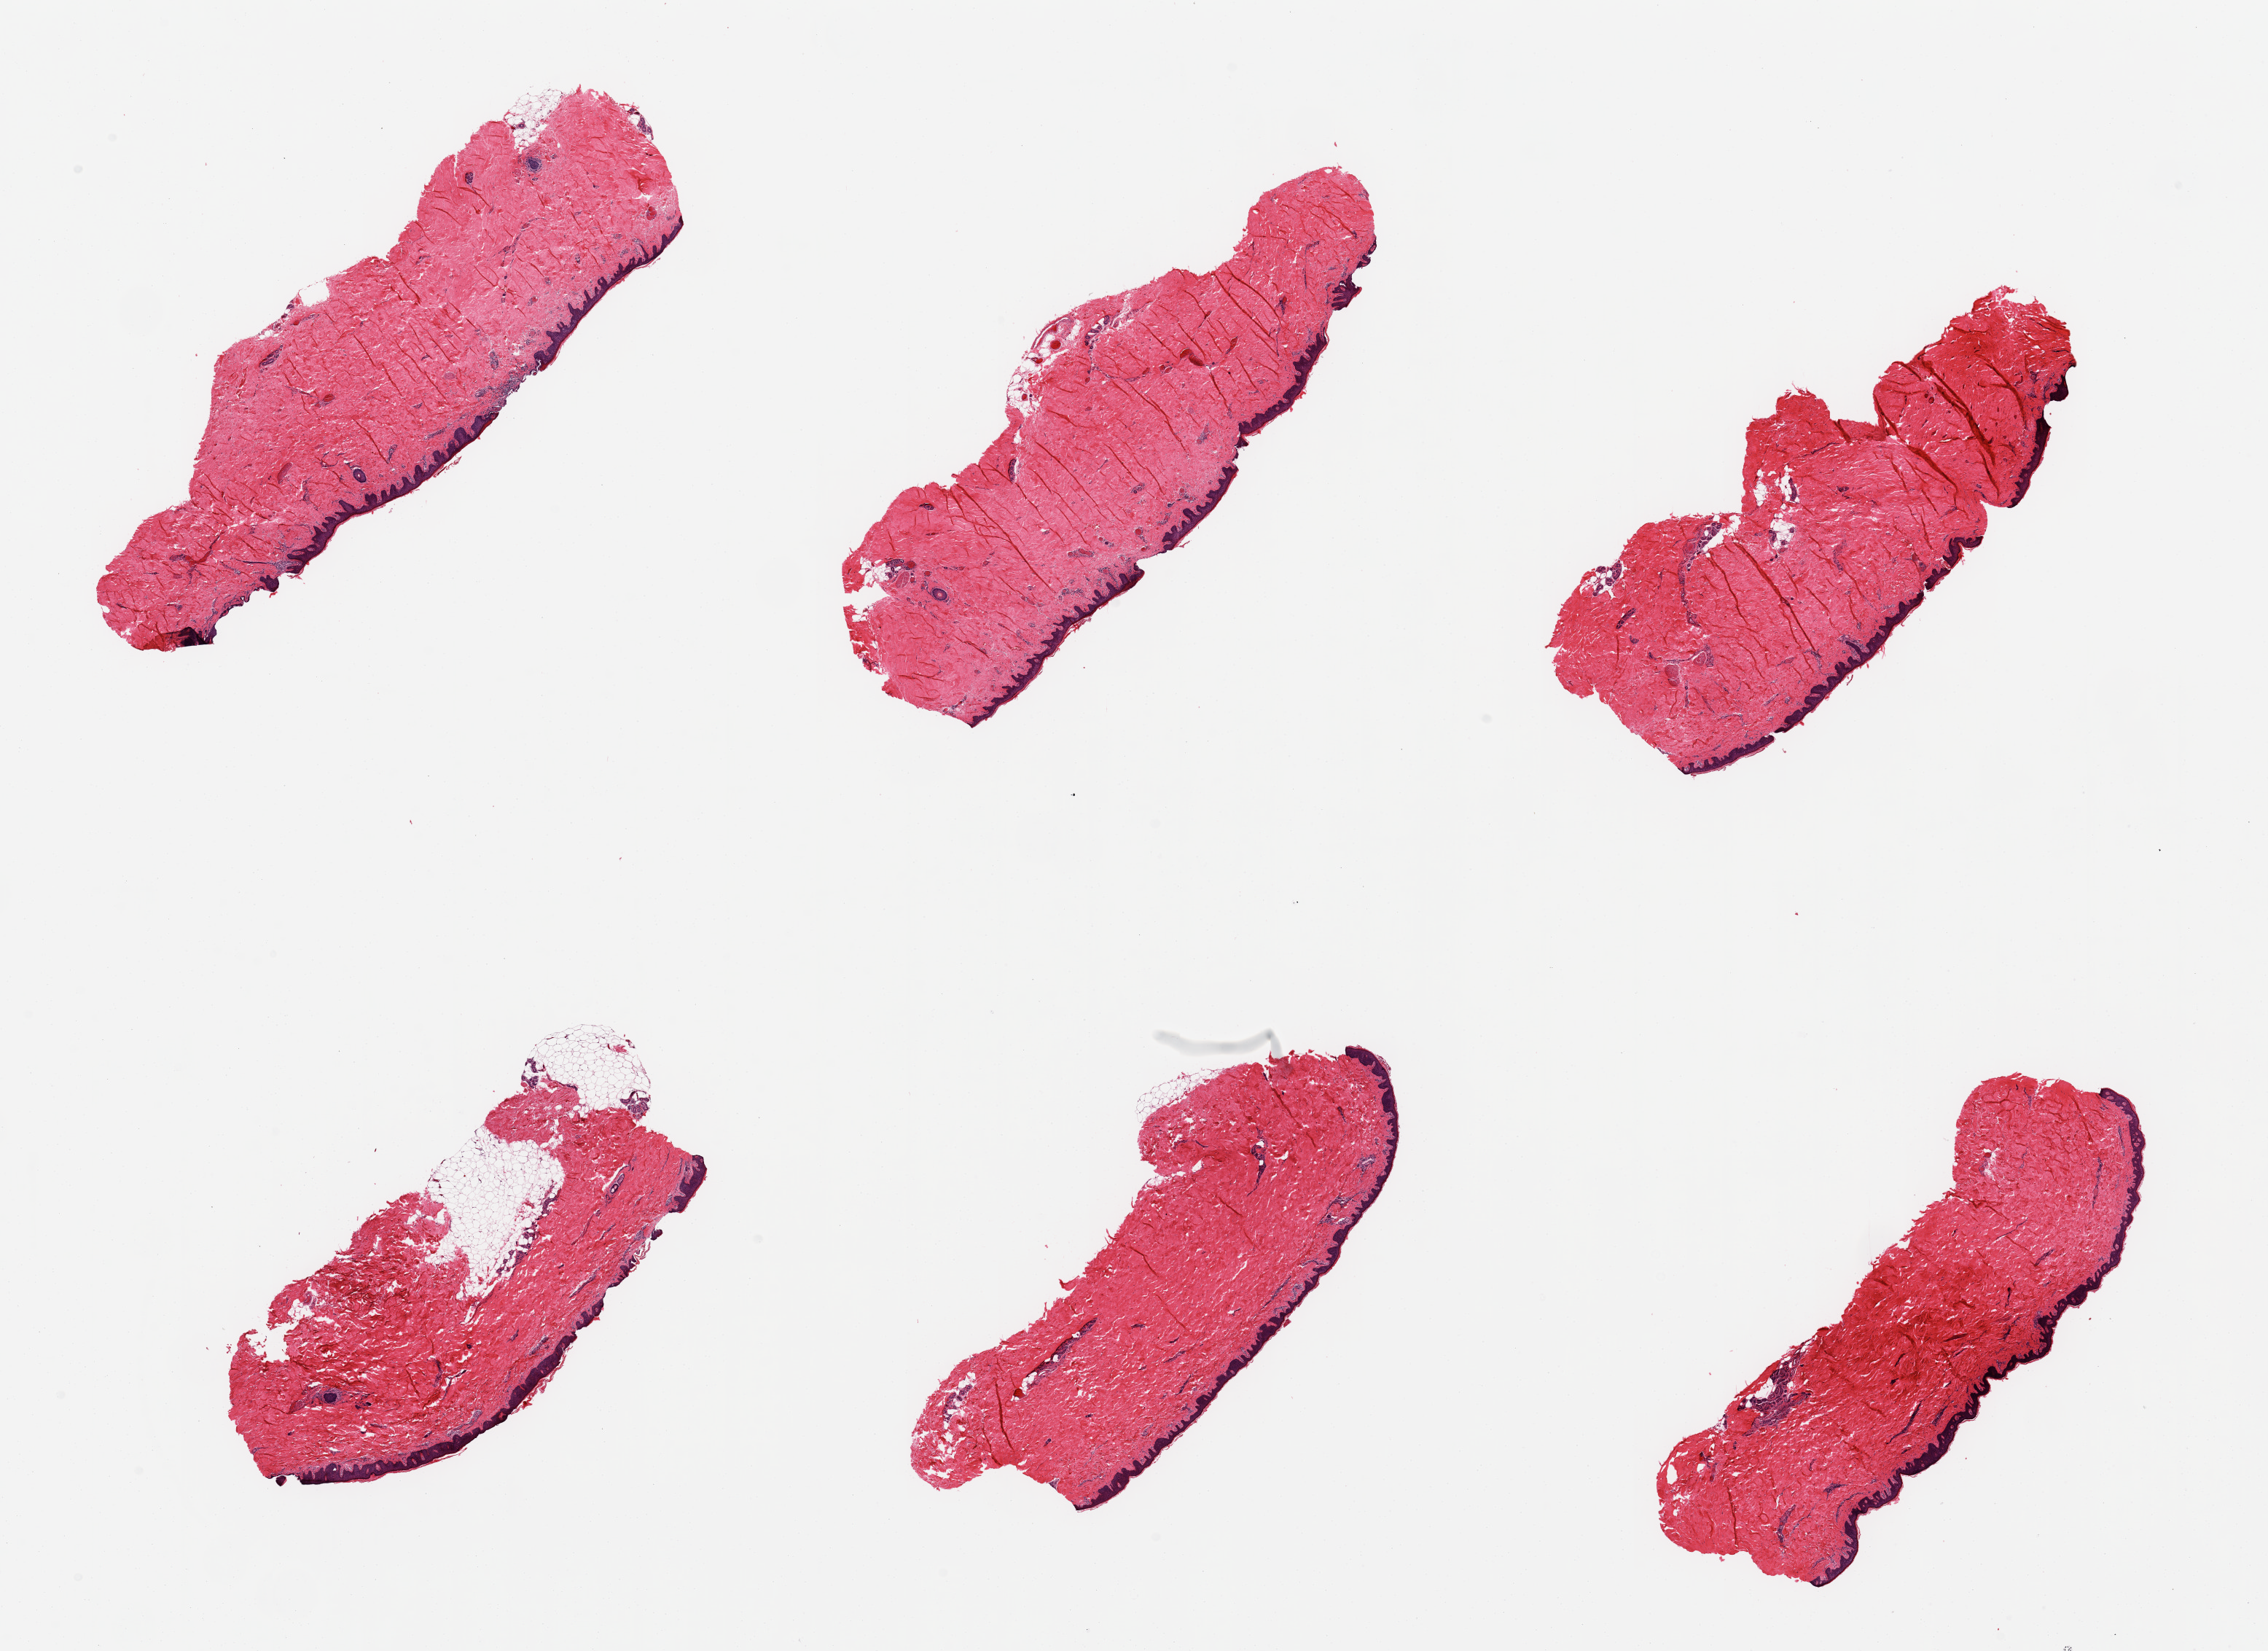
Haematoxylin and eosin whole-slide image — whole scanned area (about 24.6 x 17.9 mm) shown as a low-resolution overview; PAXgene-fixed, paraffin-embedded tissue; sampled site (target tissue): skin of suprapubic region; donor tissue sample. Female donor.
Reviewer comment on this tissue sample: 6 pieces; one piece with ~20% attached and internal fat, some parakeratosis.